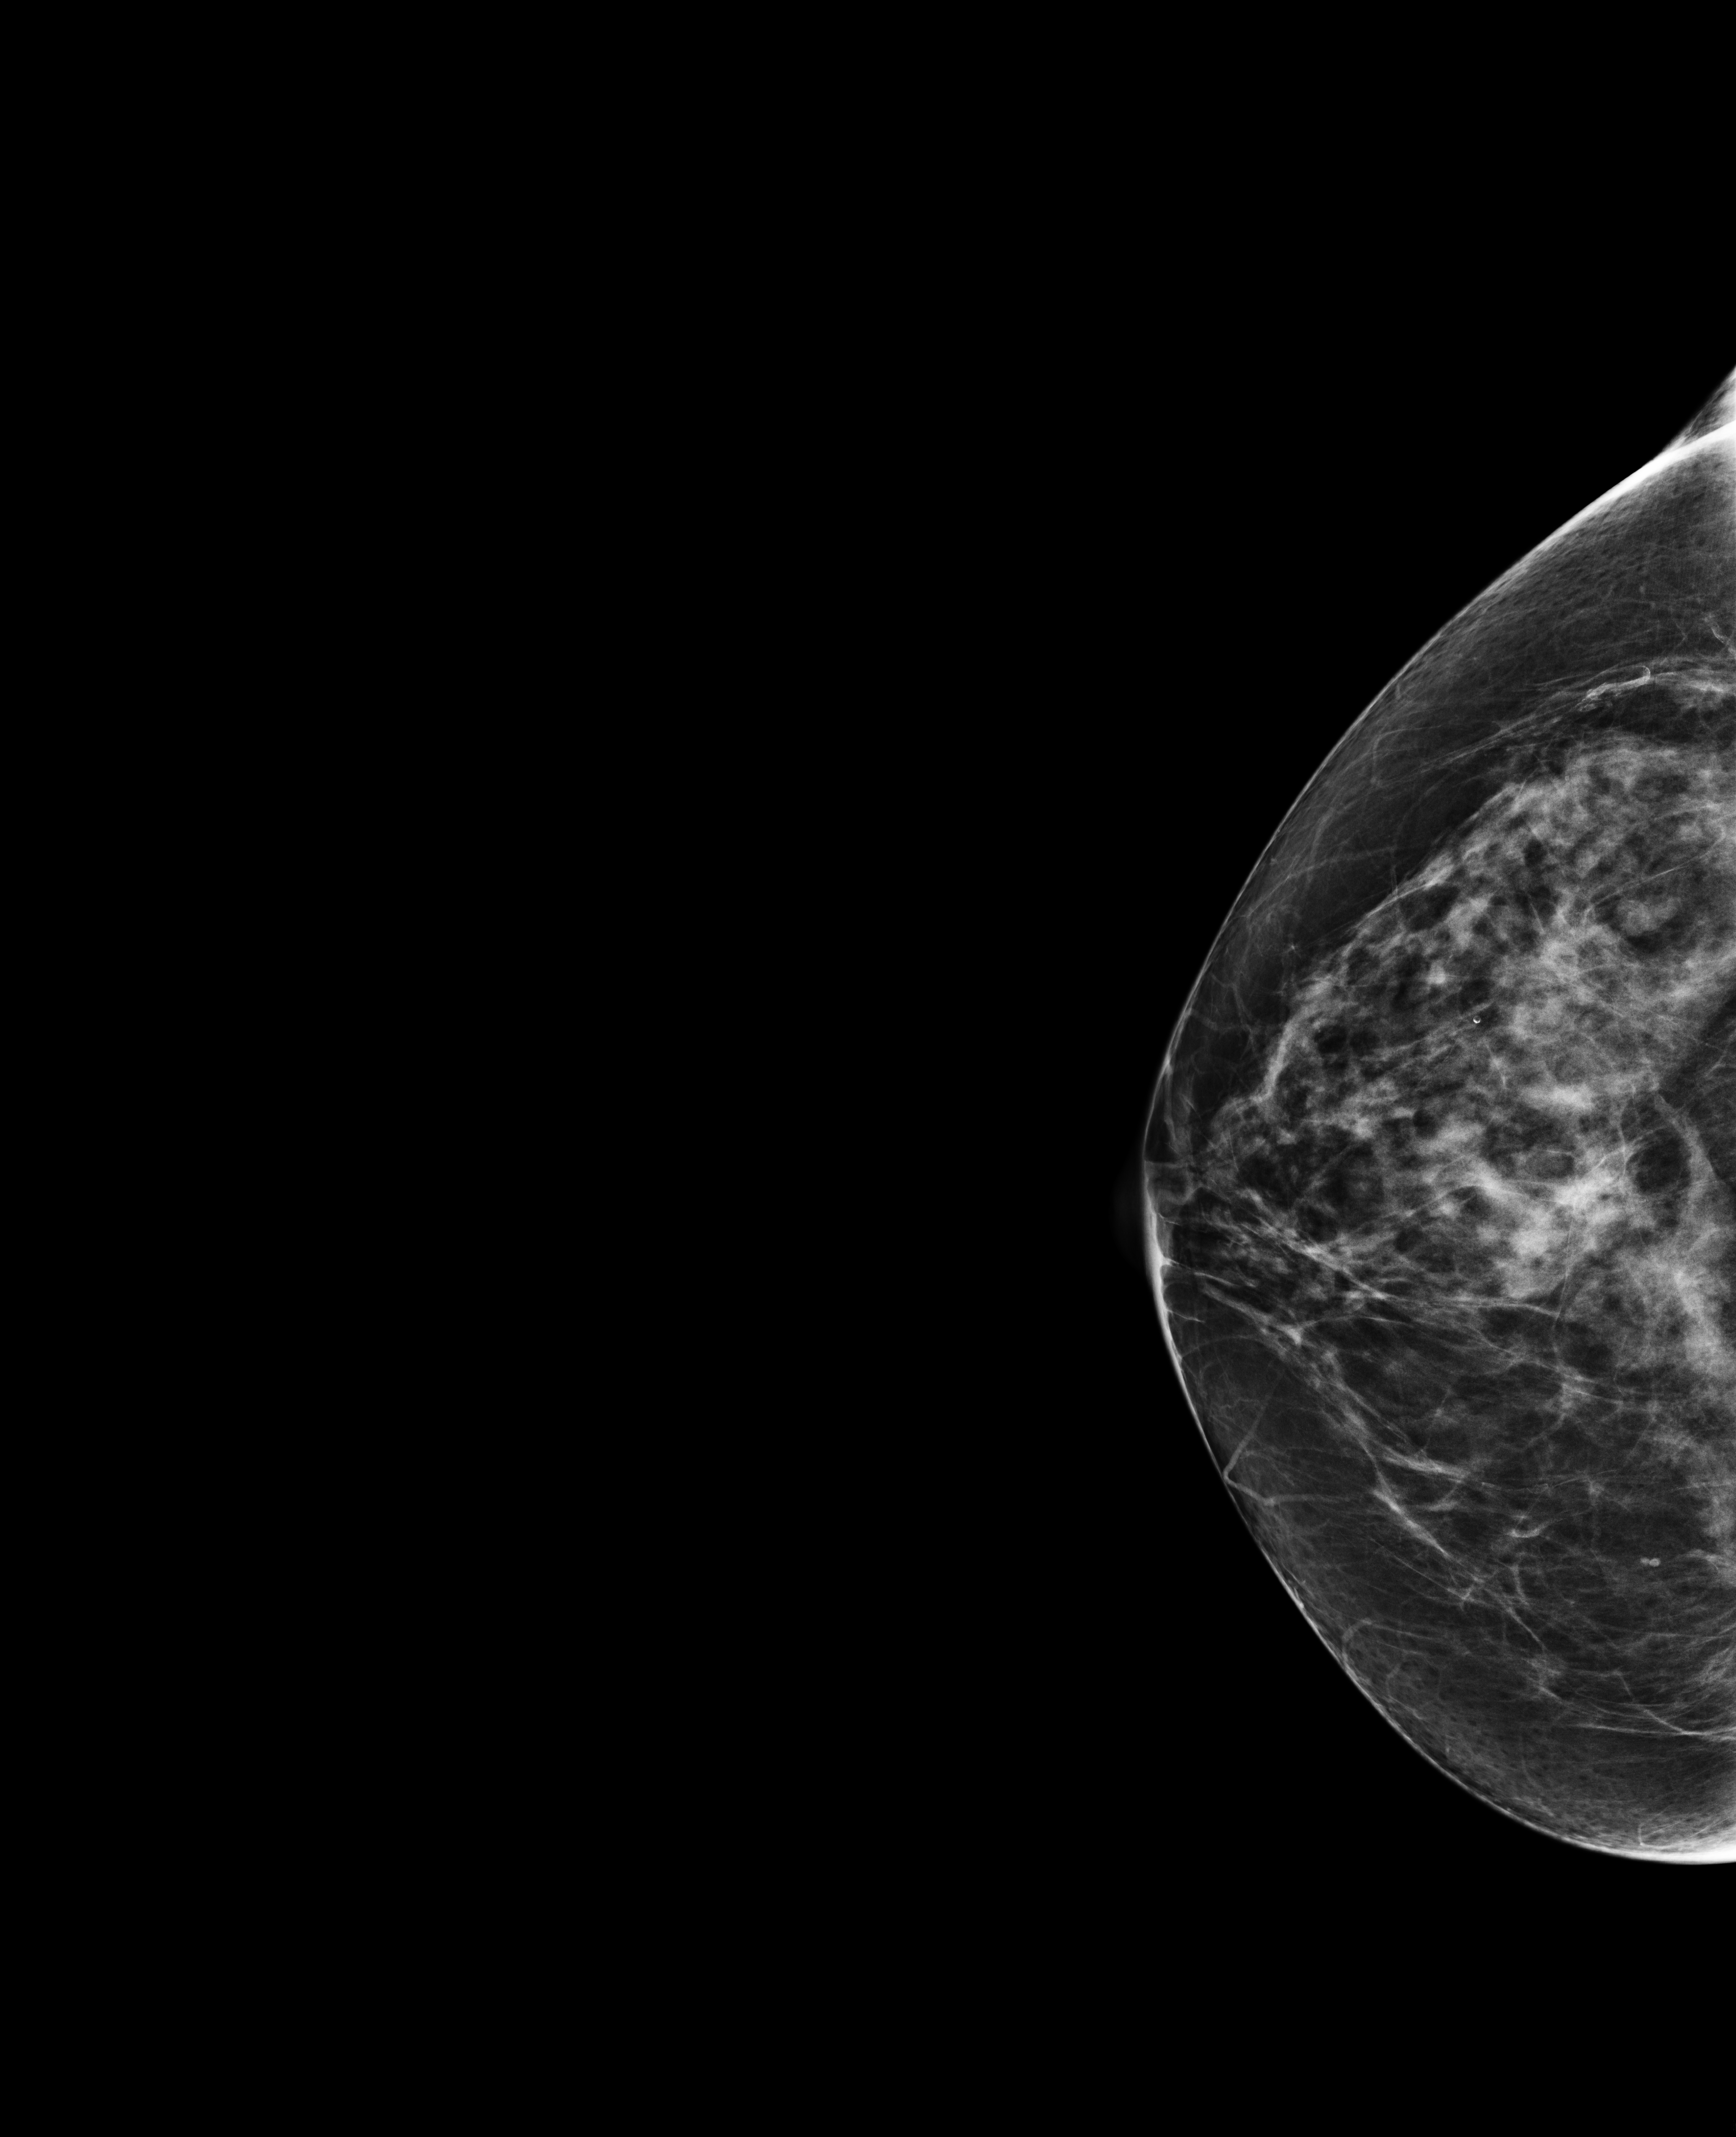
Full-field digital mammogram (FFDM); right breast; CC view; screening examination; compressed breast thickness 73 mm; system: Selenia Dimensions. Patient: female, 67 years.
BI-RADS breast density category at the screening exam (both breasts, scale 1–4): 3. Final BI-RADS assessment for this screening round (tomosynthesis exam, both breasts): category 1. Recall: no recall after this screen.